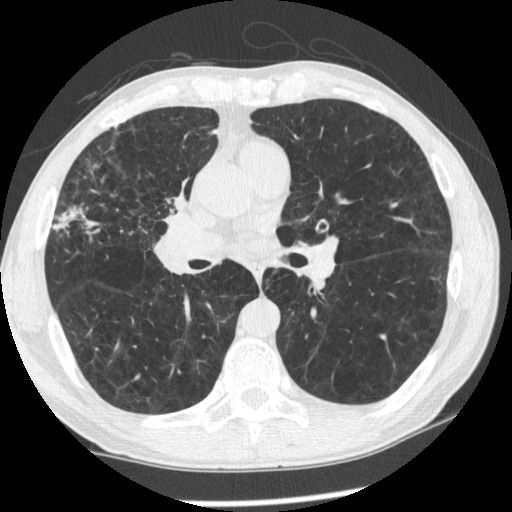
Low-dose screening chest CT, one axial slice. Lung window (W 1500 / L -600 HU). 1.25 mm slice thickness. 512 × 512 image matrix, field of view 340 × 340 mm.
Structures marked on this image (expert manual segmentation):
- lesion 1 (tumor, upper lobe of right lung): bounding box (x1, y1, x2, y2) in pixels: (171, 192, 187, 210)